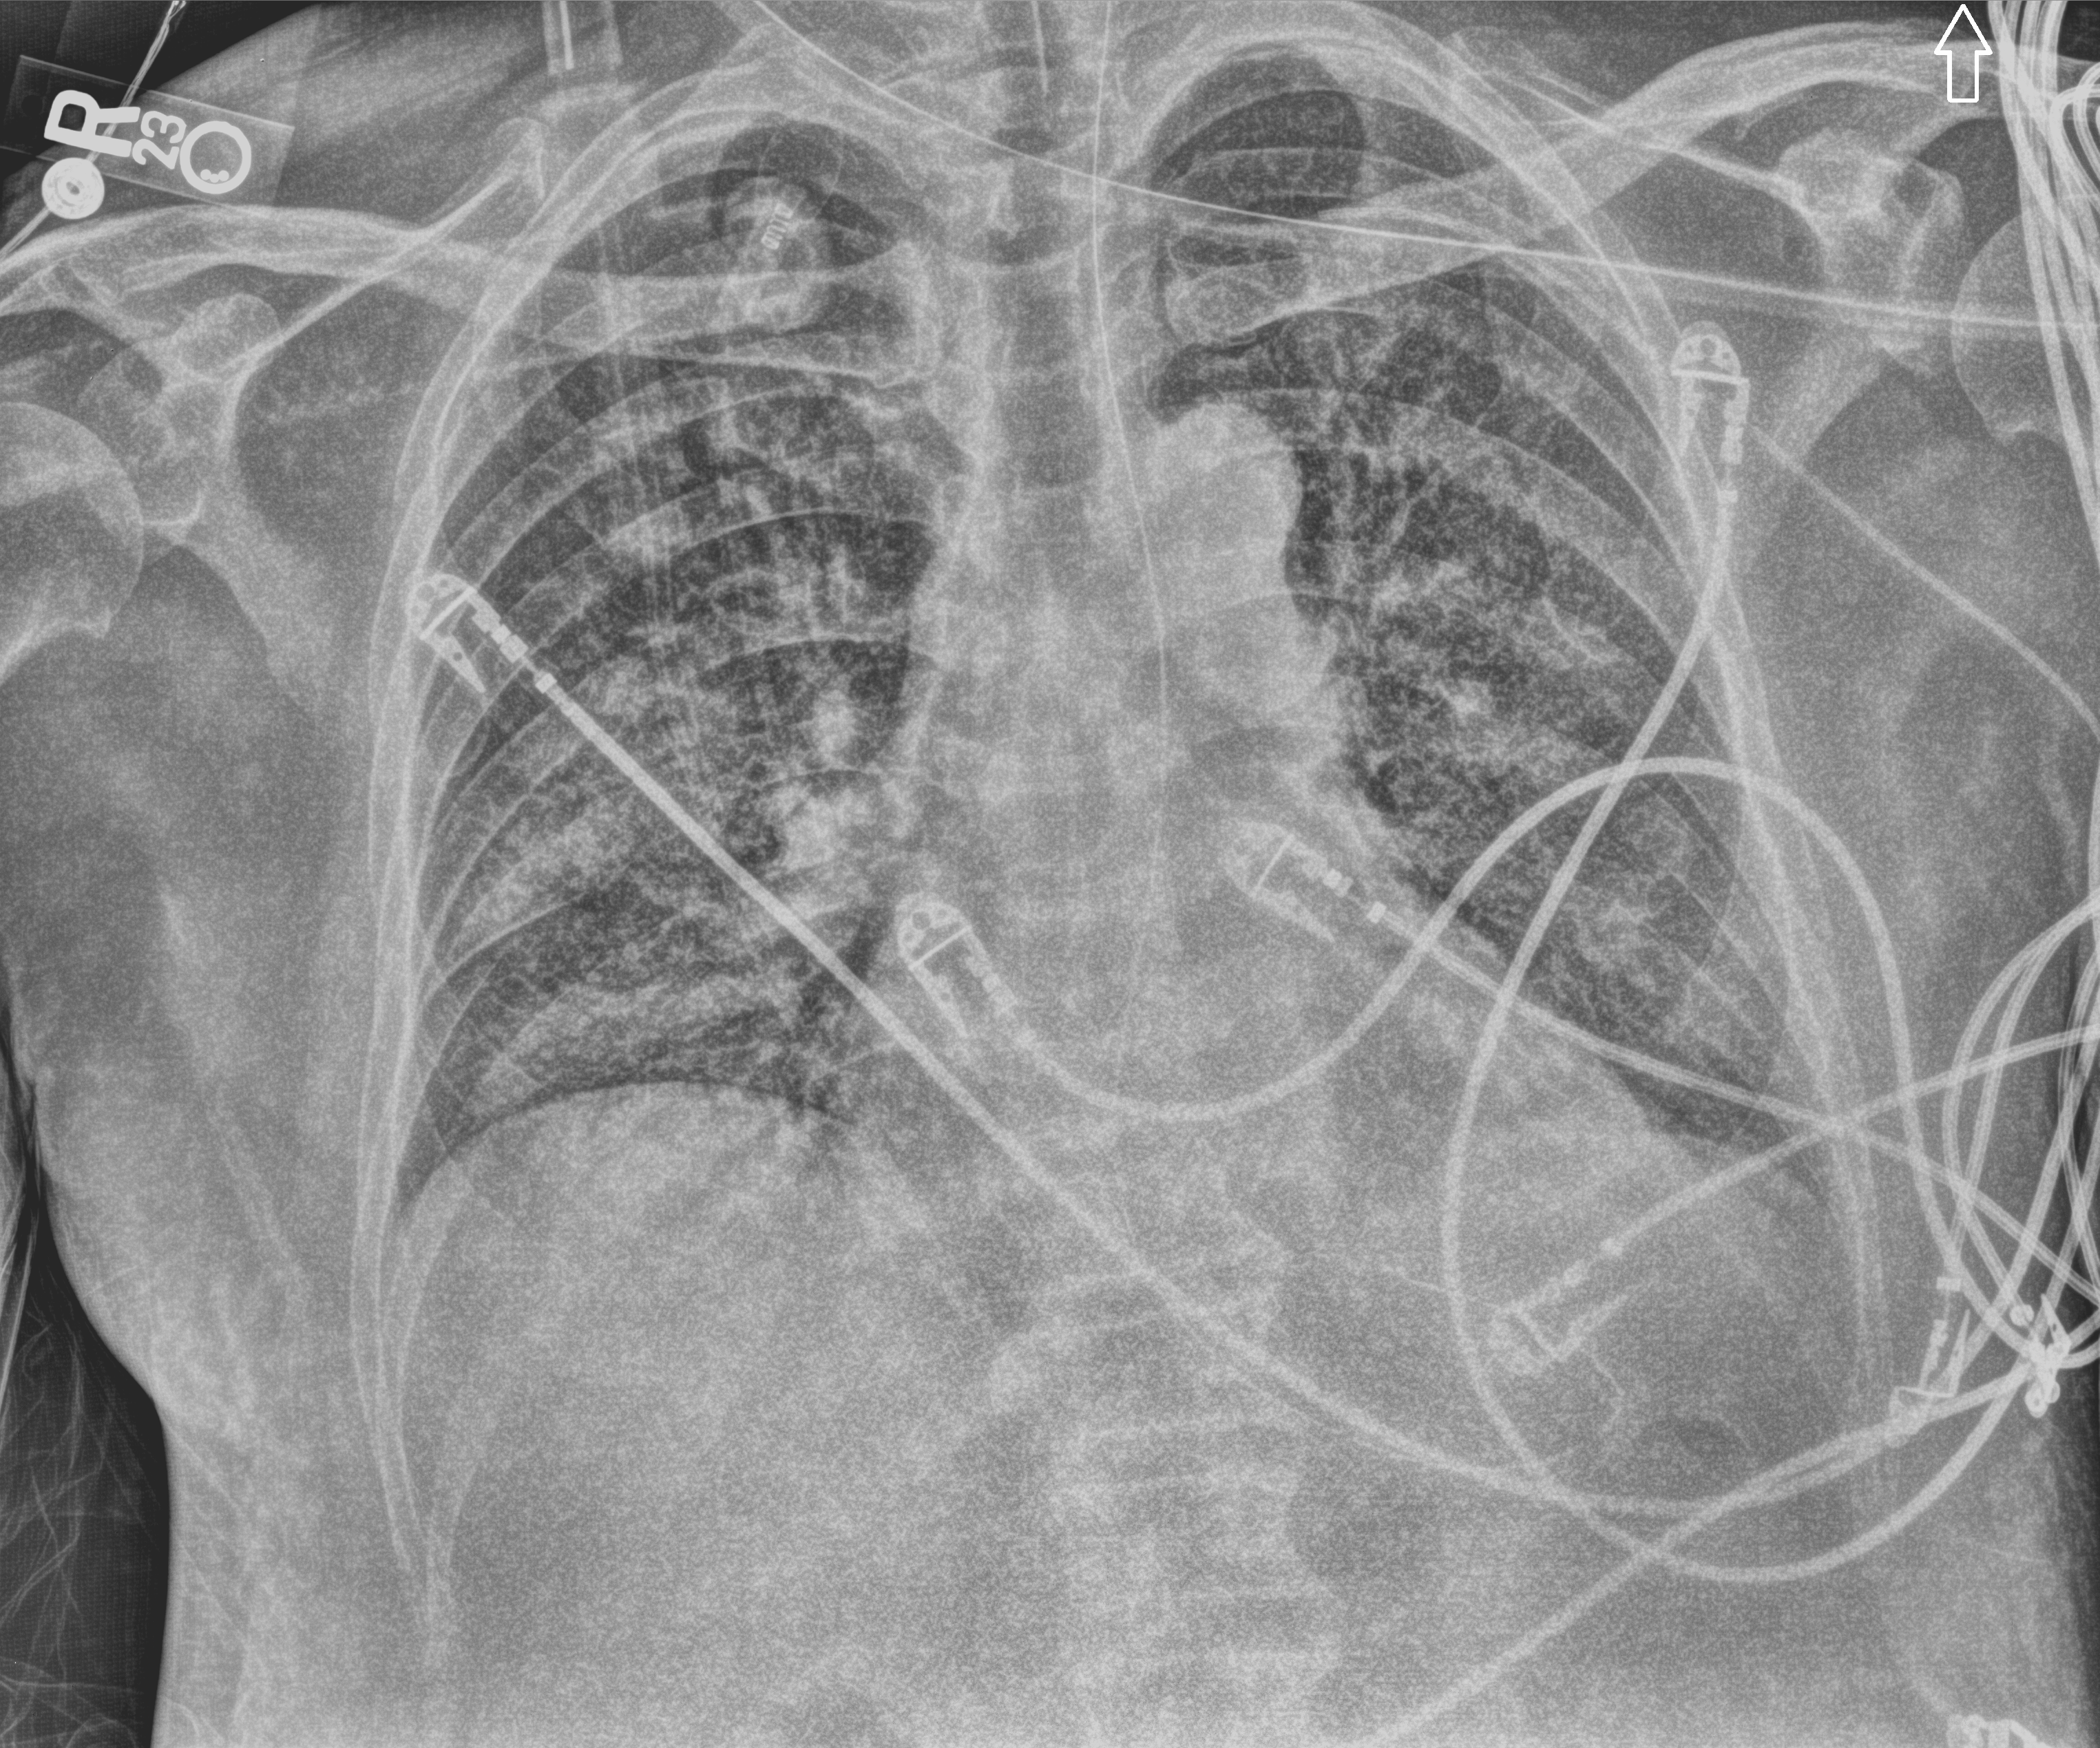
Bedside chest radiograph (computed radiography), anteroposterior (AP) projection. Patient hospitalised with COVID-19; male, aged 60–74 years.
Hospital-stay facts (about this admission, not read from this image; timing relative to this image not recorded): length of hospital stay: 14 days; admitted to intensive care during this hospital stay: yes; mechanically ventilated during this hospital stay: yes.